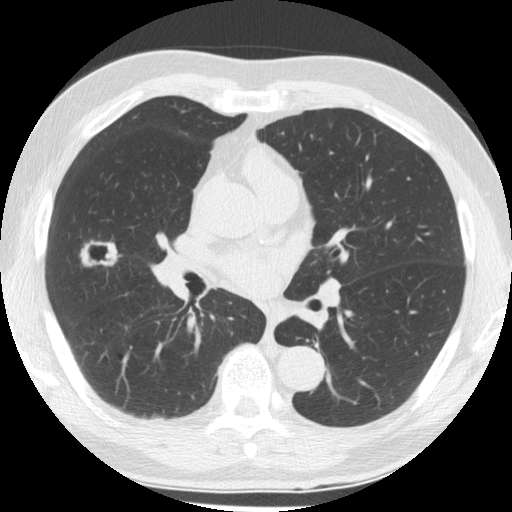
Low-dose screening chest CT, axial slice, first (baseline) screen, lung window (W 1500 / L -600 HU), 2.5 mm slice thickness, 512 × 512 image matrix. Male, age 64 years at enrolment. Former smoker at enrolment.
Expert-annotated lung lesion, box from (x=64, y=221) to (x=129, y=285) px. The screening reader recorded 2 non-calcified nodules or masses ≥4 mm on this exam; which of them this box marks is not recorded.